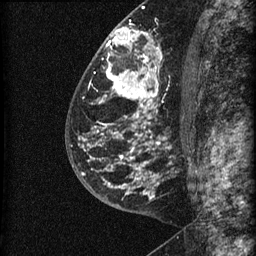
Breast MRI (dynamic contrast-enhanced), one sagittal slice. Position 37 of 60 along the scan axis. Dynamic contrast-enhanced series, image 2 of 3 at this slice position (ordered by acquisition). 1.5 T. TE 4.2 ms, TR 22.7 ms. 1.5 mm slice thickness. 256 × 256 image matrix, field of view 180 × 180 mm. Patient: female, 48 years. From the clinical record (not read from this slice): setting: breast cancer imaged before/during neoadjuvant chemotherapy; receptor status: triple-negative.
Structures marked on this image (semi-automatically segmented with operator editing):
- analysis volume of interest (the breast-tissue region the enhancement analysis was run in; not a lesion): box from (x=81, y=23) to (x=186, y=202) px
- tumour enhancement mask (voxels above the 90 % enhancement threshold inside the analysis volume of interest): (x=81, y=27)–(x=166, y=194)